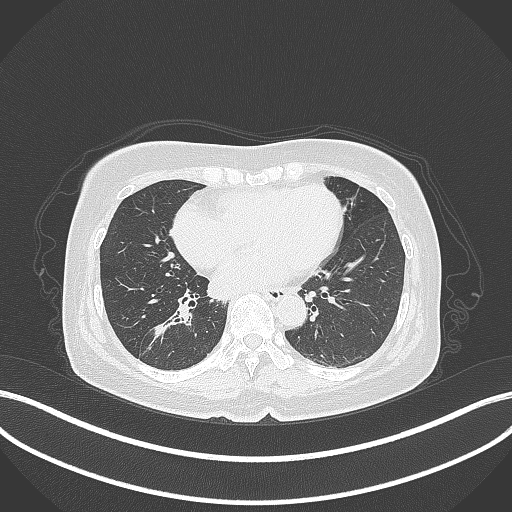
Chest CT, one axial slice; slice 163 of 429 in the series (ordered by position); reconstruction kernel B70f; lung window (W 1500 / L -600 HU); 512 × 512 image matrix, field of view 400 × 400 mm. Female patient, age 67 years. Case-level facts recorded for this patient, not image findings: clinical TNM (as recorded): T1c N1 M0; histopathological grade: G2-3.
Outlined on this slice (bounding box drawn by a radiologist):
- lung tumour (recorded histology: adenocarcinoma): bounding box (x1, y1, x2, y2) in pixels: (143, 300, 197, 358)